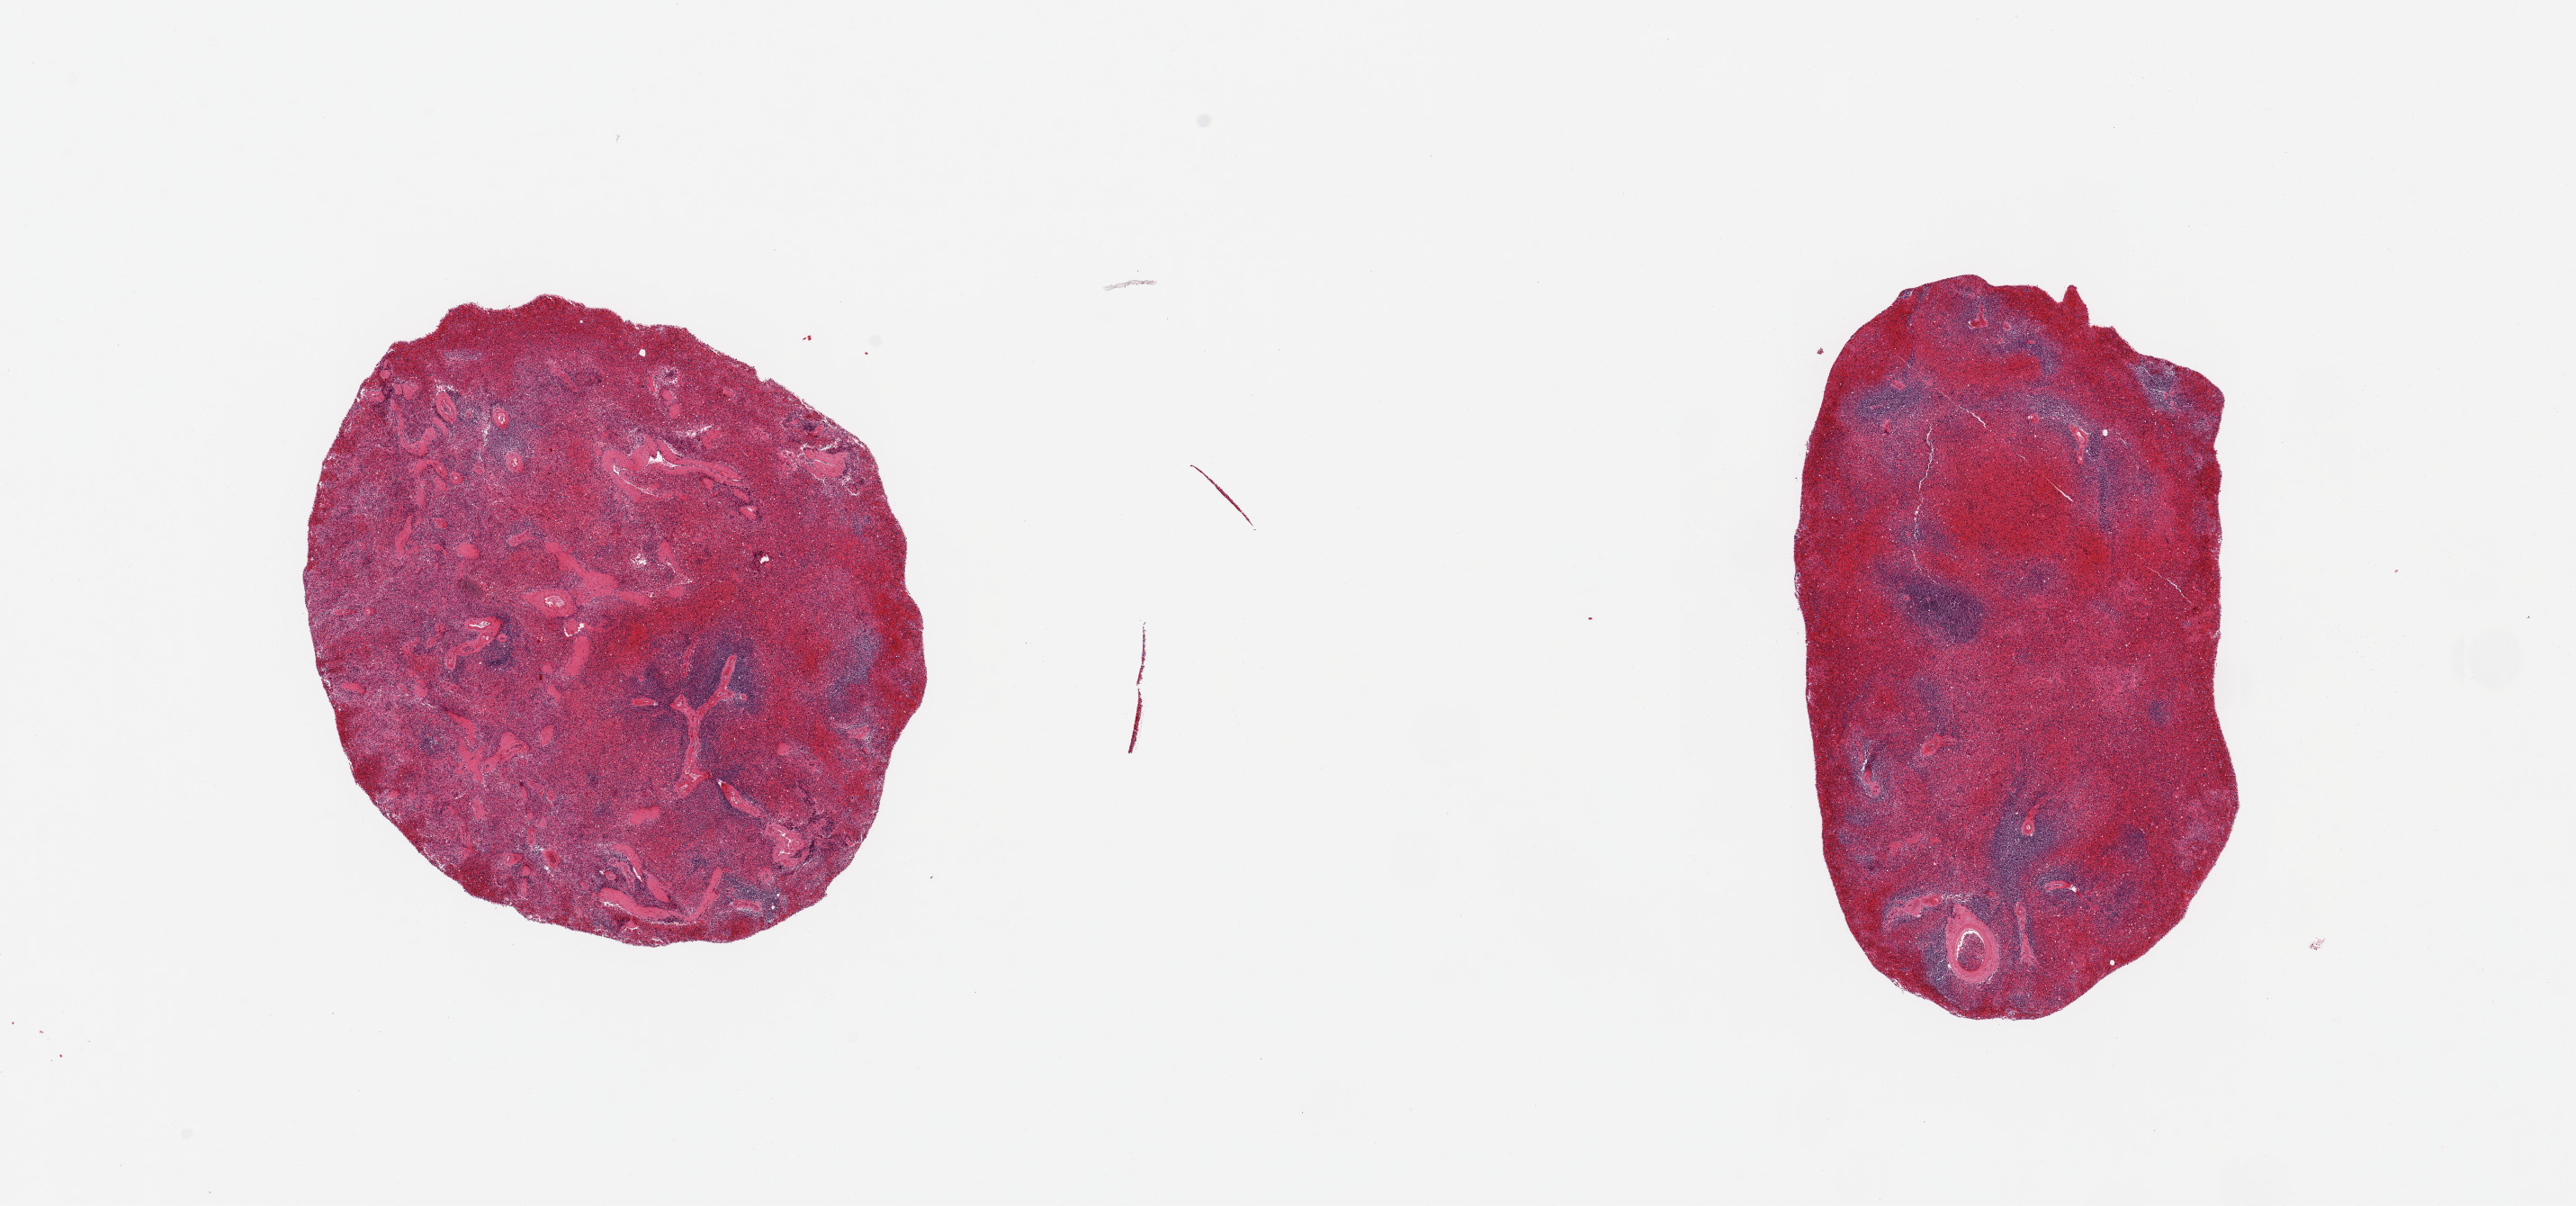
Digitized hematoxylin and eosin (H&E)-stained section, brightfield, a low-resolution overview of the entire scanned area, about 22.6 x 10.6 mm (acquisition: 20x scan). PAXgene-fixed paraffin-embedded (PFPE) section. Section of spleen (target tissue). Donor tissue sample. Donor: female.
Review note (as recorded): 2 pieces; severe congestion.